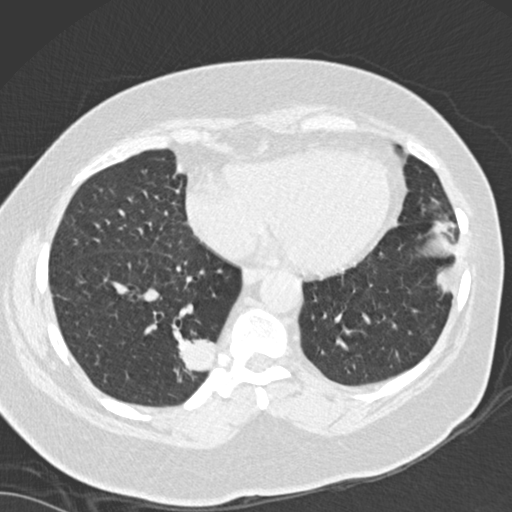
Low-dose screening chest CT, one axial slice; slice 54 of 162 in the series (ordered by position); 120 kVp; lung window (W 1500 / L -600 HU); 2 mm slice thickness; 512 × 512 image matrix.
Outlined on this slice (expert manual segmentation):
- lesion 1 (tumor, lower lobe of right lung): bounding box [x1, y1, x2, y2] px = [178, 339, 215, 374]